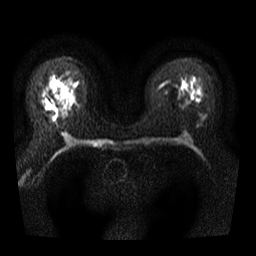
Breast MRI, one axial slice. Slice 21 of 40 in the series (ordered by position). Diffusion-weighted series; image 2 of 4 stored at this slice position (different b-values; order by instance number). 3 T. 5 mm slice thickness. 256 × 256 image matrix, field of view 300 × 300 mm. Female patient.
Outlined on this slice (expert manual segmentation):
- tumour on diffusion-weighted imaging: bounding box (x1, y1, x2, y2) in pixels: (50, 113, 57, 123)